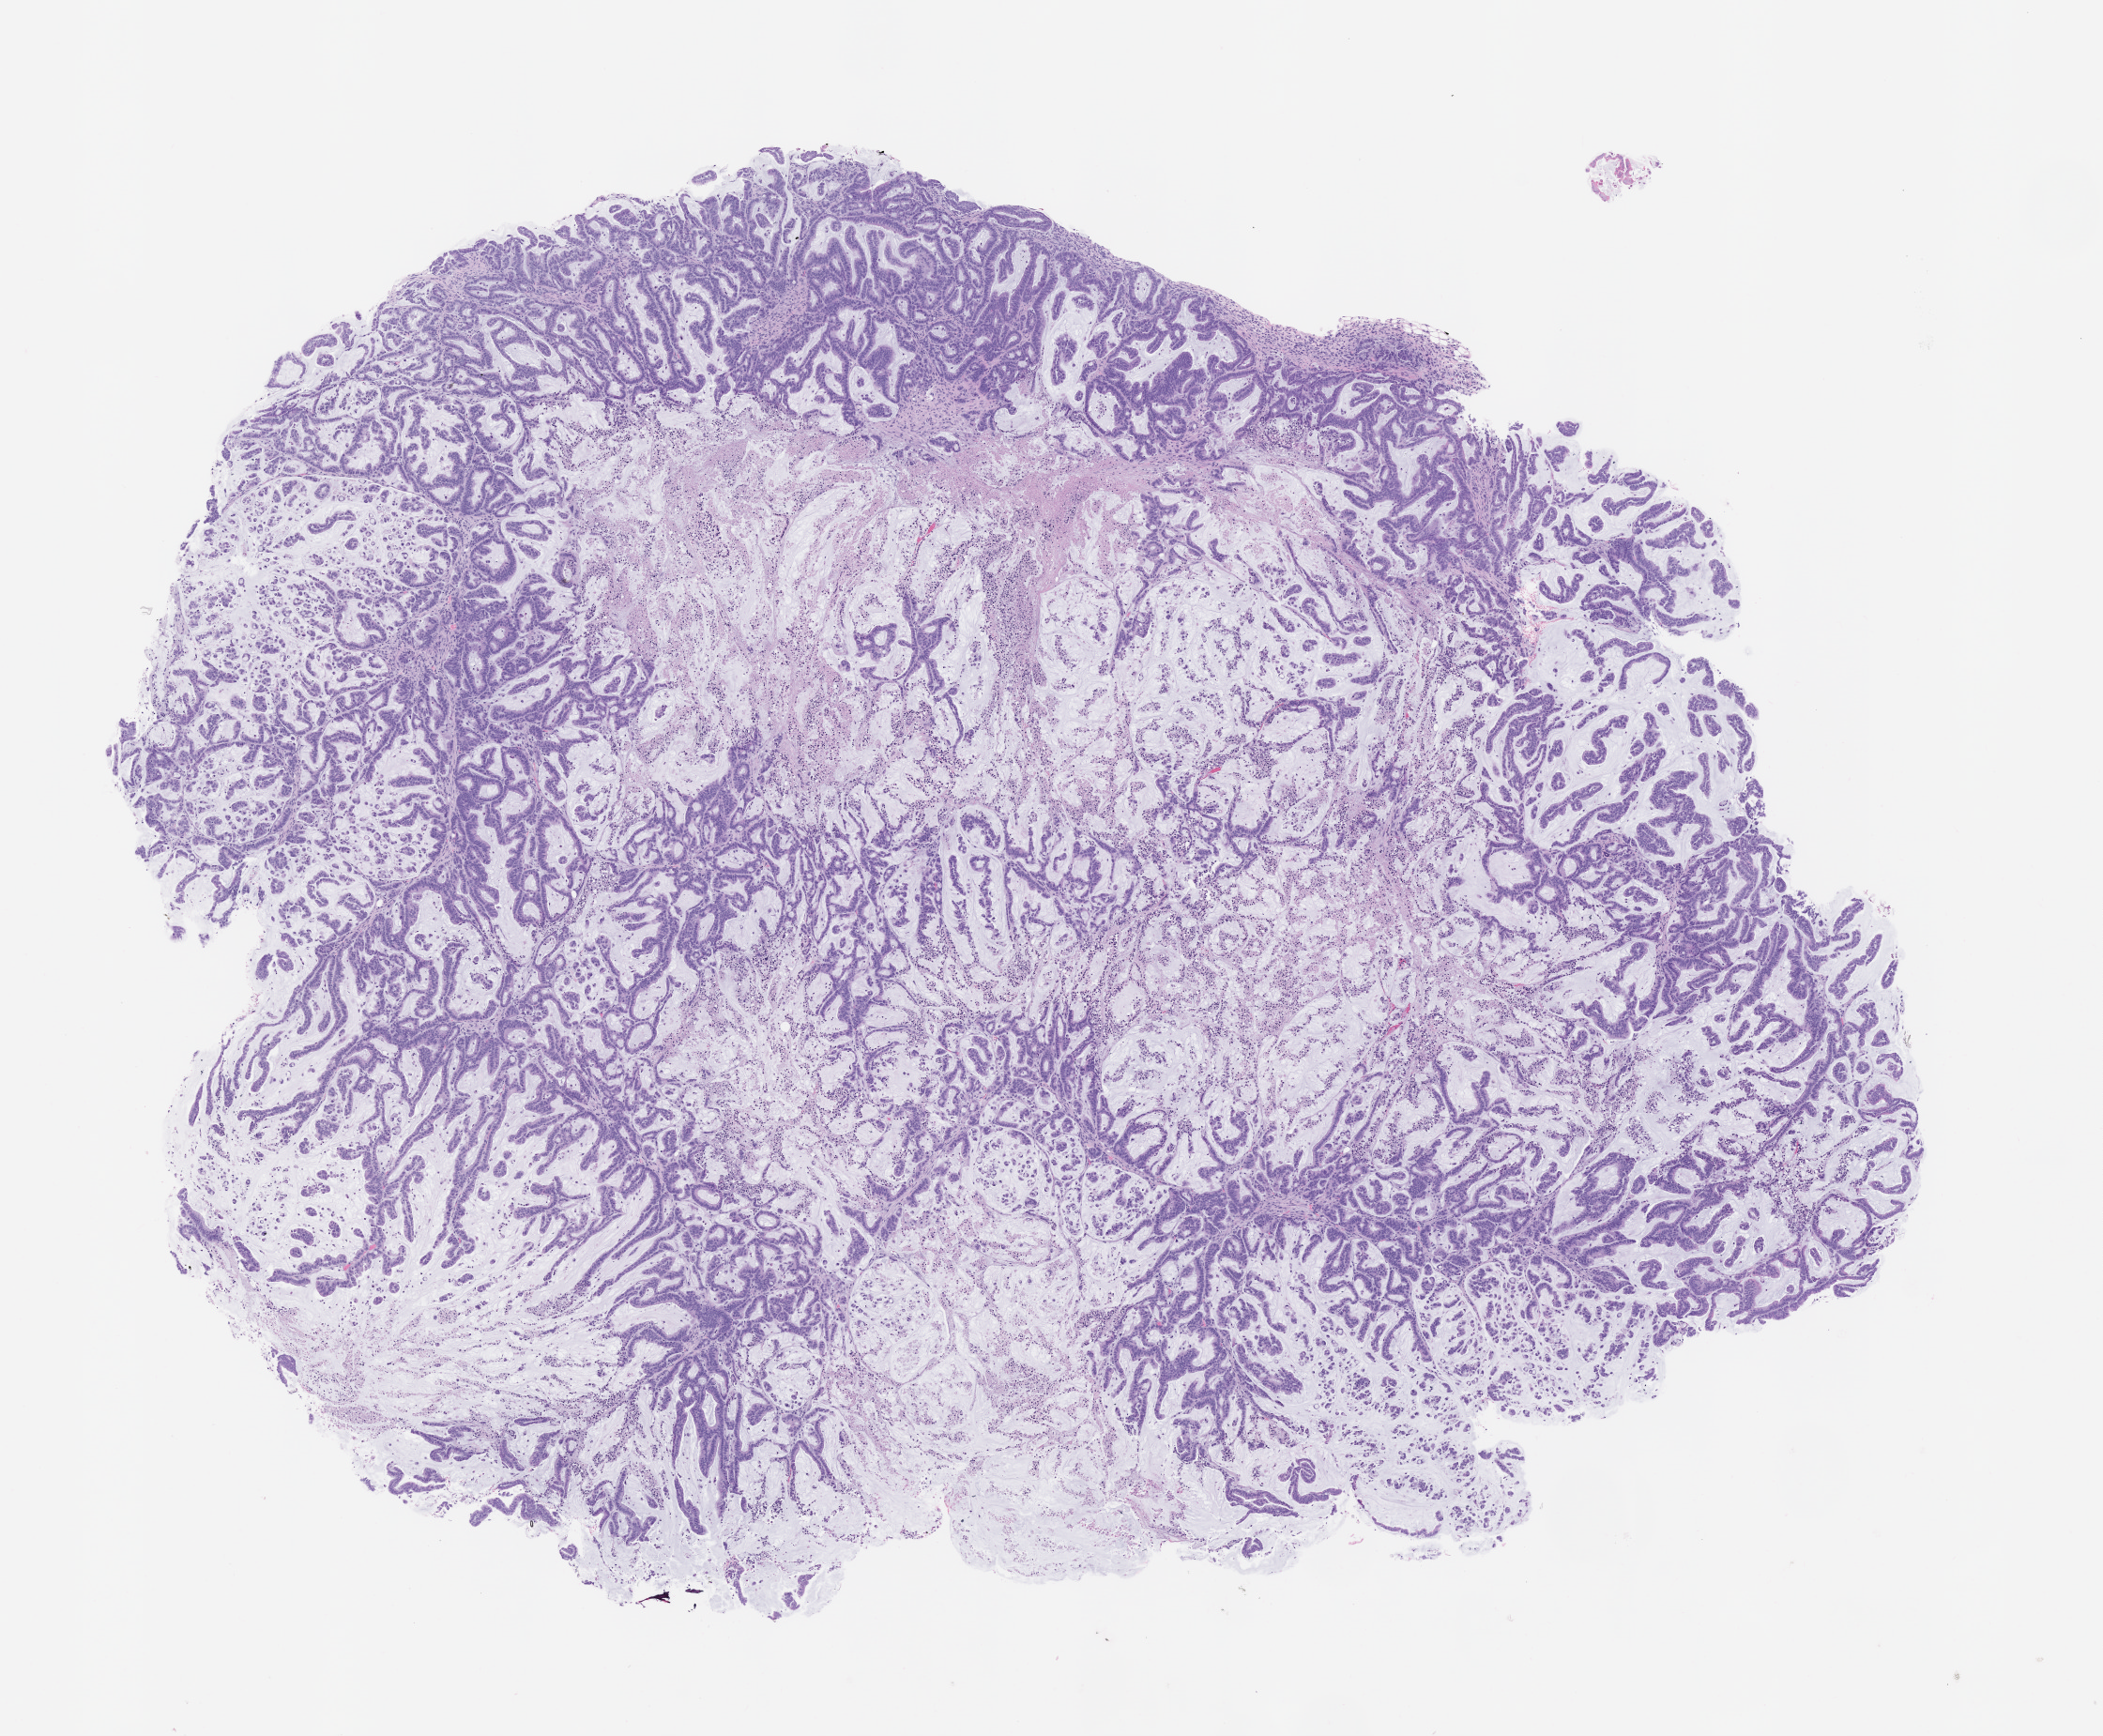
Whole-slide image, haematoxylin and eosin: patient-derived xenograft (human tumor grown in a mouse), passage 1, shown as a low-resolution overview of the whole scanned area (about 9.0 x 7.4 mm), formalin-fixed paraffin-embedded section, tumor site category: colon.
Originating patient diagnosis: Colon Adenocarcinoma.